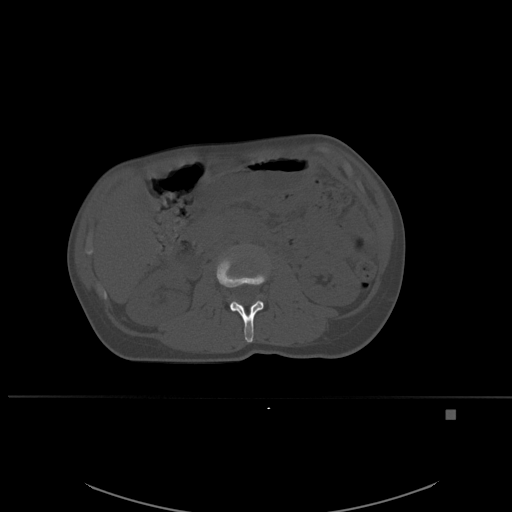
CT including the spine, one axial slice. Position 229 of 537 along the scan axis. Bone window (W 1800 / L 400 HU). 1.5 mm slice thickness. 512 × 512 image matrix. Patient: female, 45 years. From the clinical record (not read from this slice): primary cancer: lung.
Structures marked on this image (semi-automatically segmented with operator editing):
- L2 vertebra: box from (x=216, y=248) to (x=269, y=343) px
- L3 vertebra: (x=236, y=246)–(x=245, y=249)